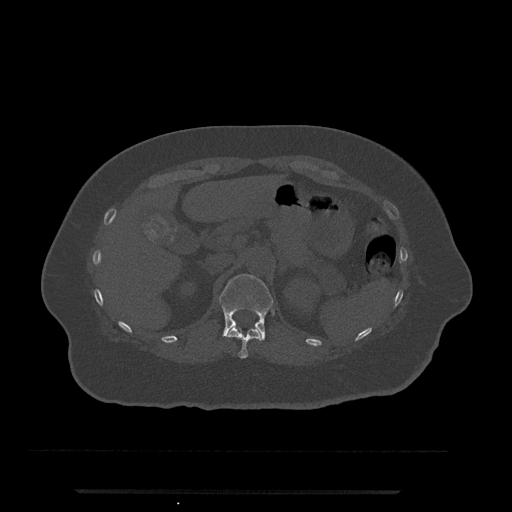
CT including the spine, one axial slice; slice 194 of 797 in the series (ordered by position); 120 kVp; bone window (W 1800 / L 400 HU); 0.5 mm slice thickness; 512 × 512 image matrix, field of view 440 × 440 mm. Female patient, age 51 years. Case-level facts recorded for this patient, not image findings: primary cancer: neuro; vertebrae with lytic lesions (as recorded): T8.
Annotated regions visible in this slice (semi-automatically segmented with operator editing):
- T11 vertebra: box from (x=226, y=327) to (x=261, y=359) px
- T12 vertebra: (x=219, y=274)–(x=274, y=341)